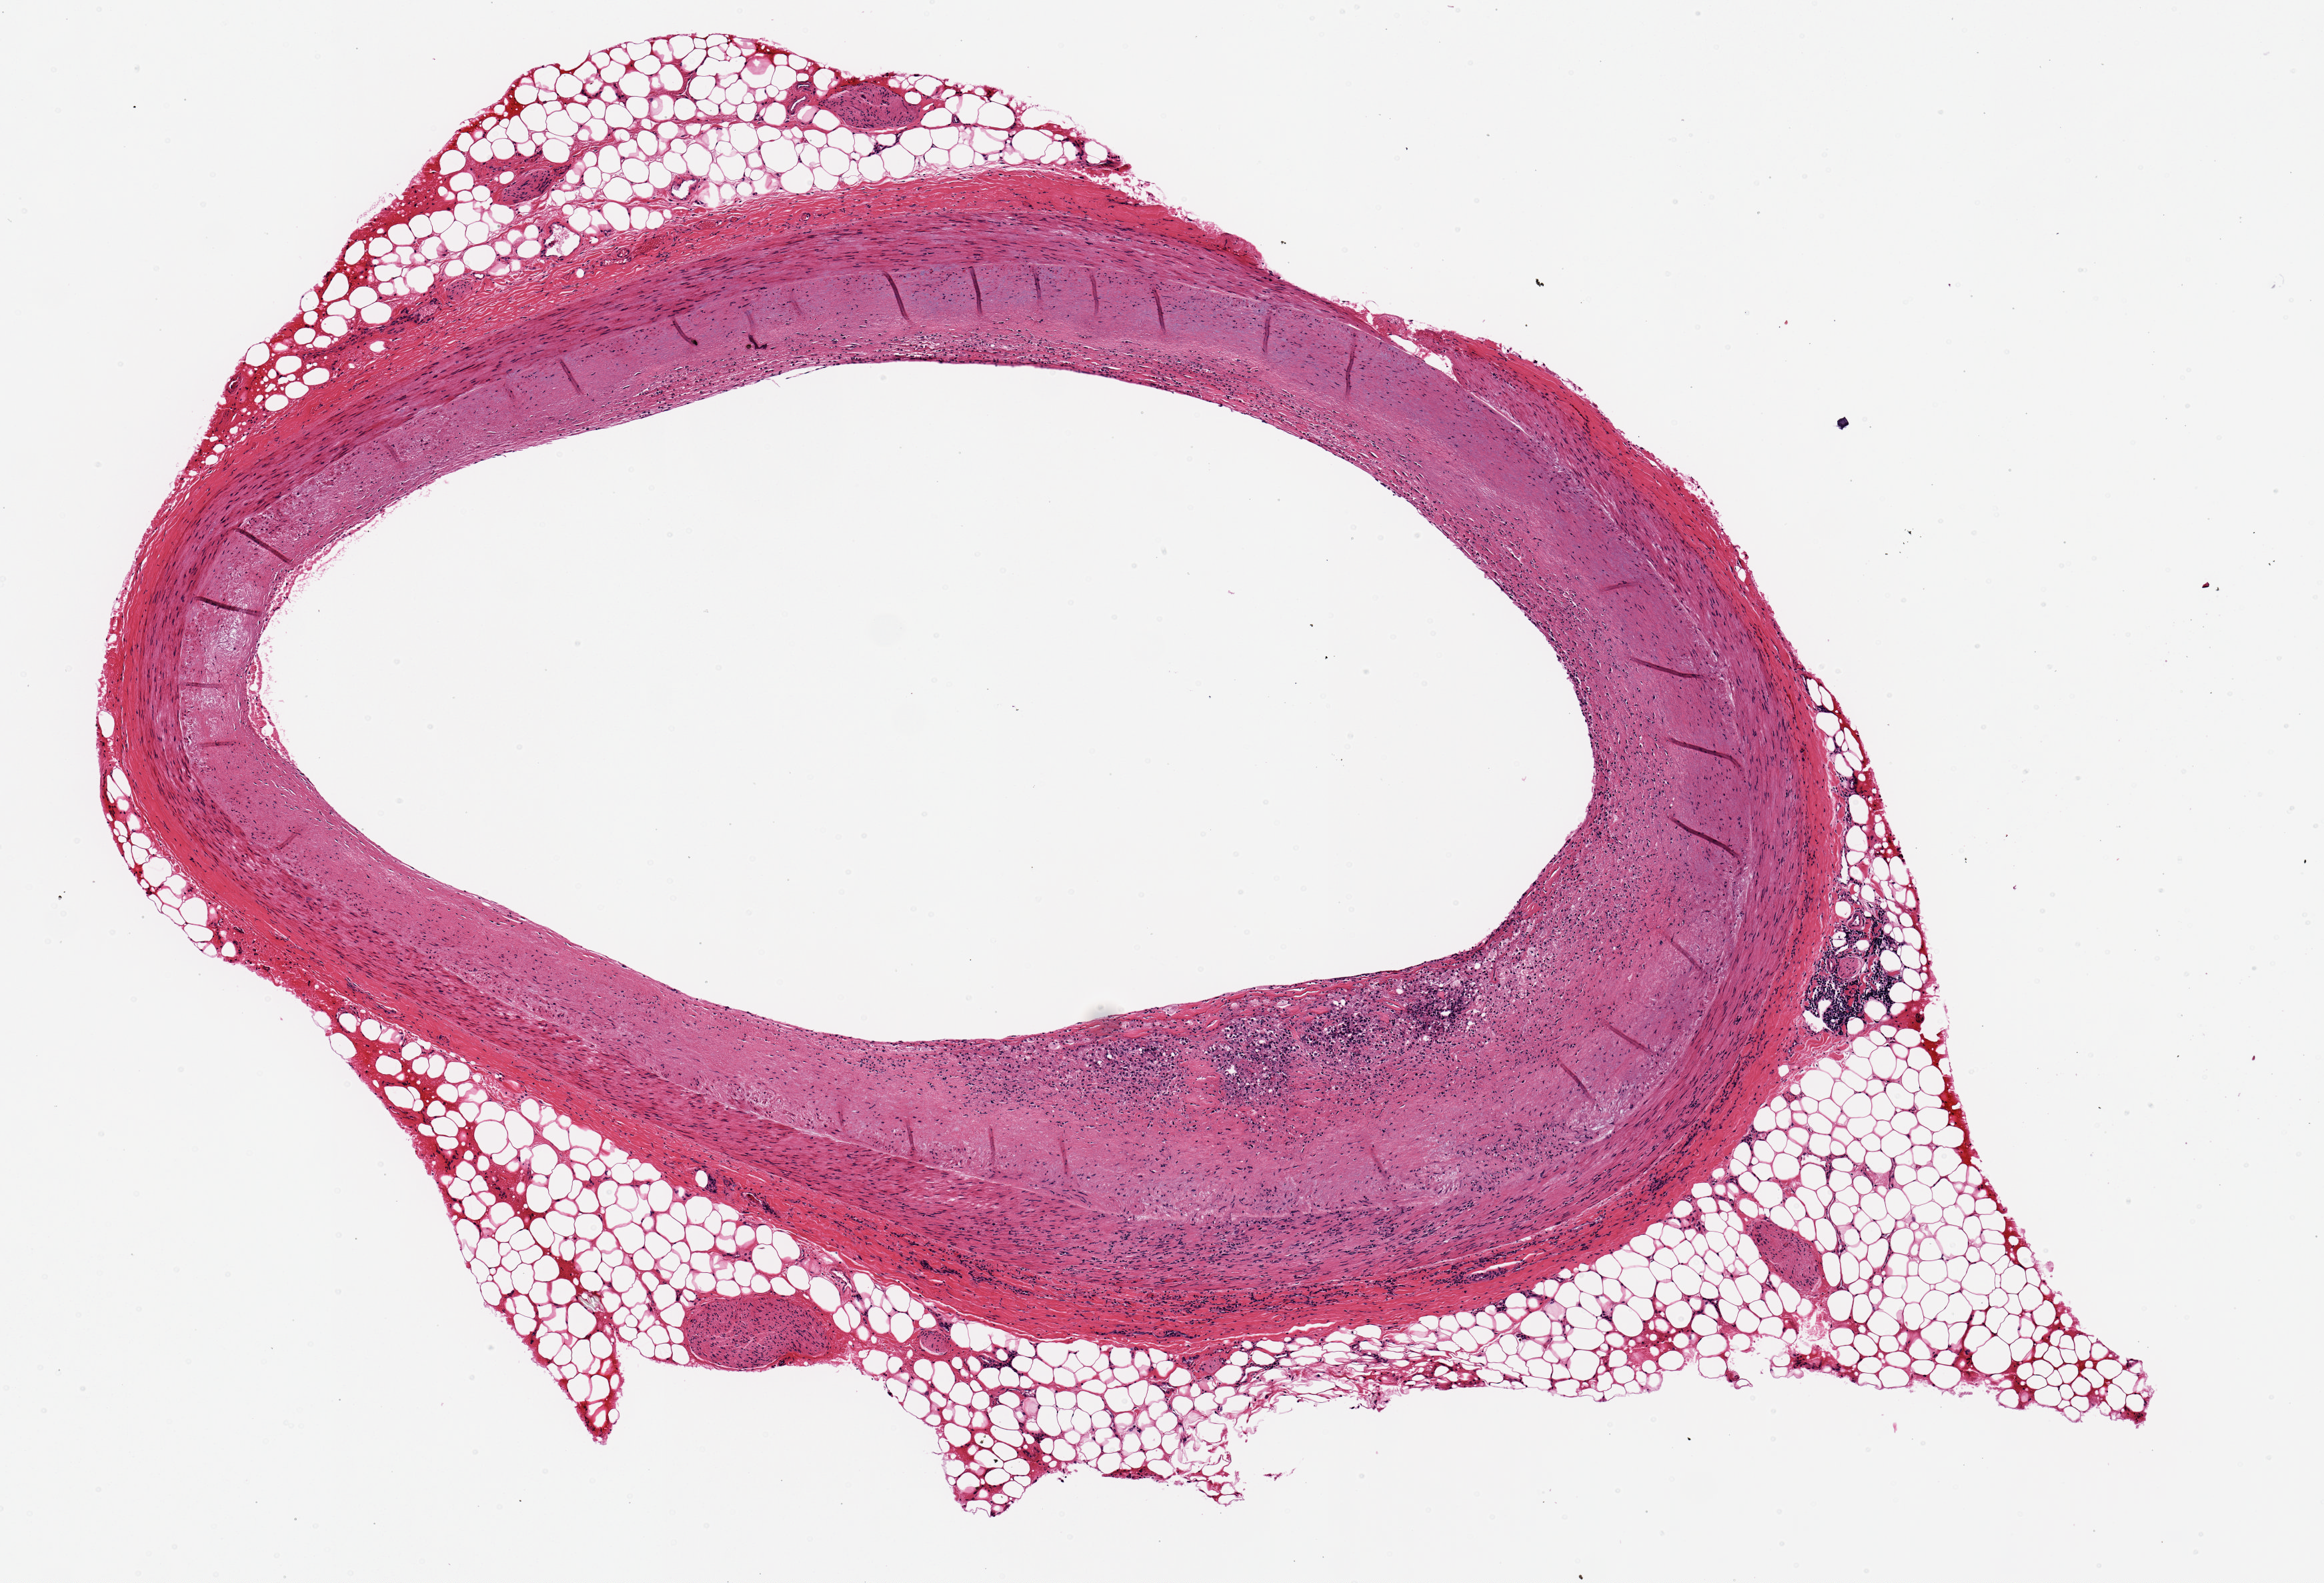
Hematoxylin and eosin (H&E) whole-slide image, a low-resolution overview of the entire scanned area, about 6.9 x 4.7 mm, PAXgene-fixed, paraffin-embedded tissue, section of coronary artery (target tissue), donor tissue sample. Donor sex: male.
- pathologist's review note for this sample: eccentric plaque, wide lumen